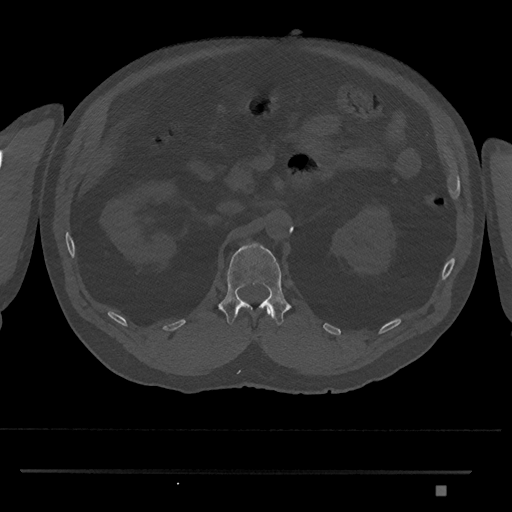
CT including the spine, one axial slice. Position 833 of 1134 along the scan axis. Reconstruction kernel Br40s/3. 120 kVp. Bone window (W 1800 / L 400 HU). 0.5 mm slice thickness. 512 × 512 image matrix, field of view 429 × 429 mm. Male patient, age 65 years. Case-level facts recorded for this patient, not image findings: primary cancer: prostate.
Structures marked on this image (semi-automatically segmented with operator editing):
- L1 vertebra: bounding box <218,242,291,326> (left, top, right, bottom; pixels)
- T12 vertebra: <267,309,272,317>